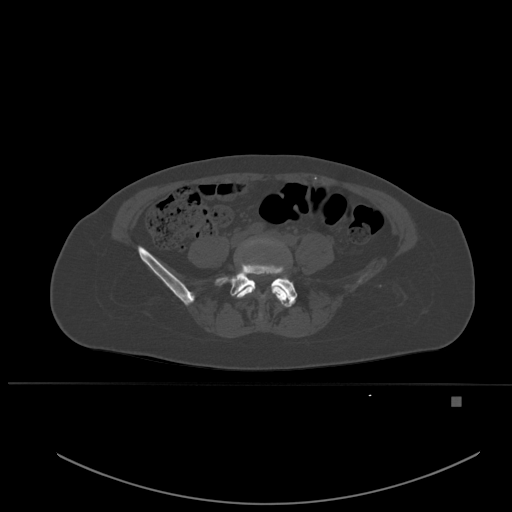
CT including the spine, one axial slice; slice 161 of 651 in the series (ordered by position); bone window (W 1800 / L 400 HU); 1.5 mm slice thickness; 512 × 512 image matrix. Patient: female, 49 years. Case-level facts recorded for this patient, not image findings: primary cancer: breast; vertebrae with lytic lesions (as recorded): L3, T12, L4.
Annotated regions visible in this slice (semi-automatic segmentation, software-assisted and operator-edited):
- L4 vertebra: box from (x=236, y=239) to (x=291, y=316) px
- L5 vertebra: (x=214, y=259)–(x=298, y=307)